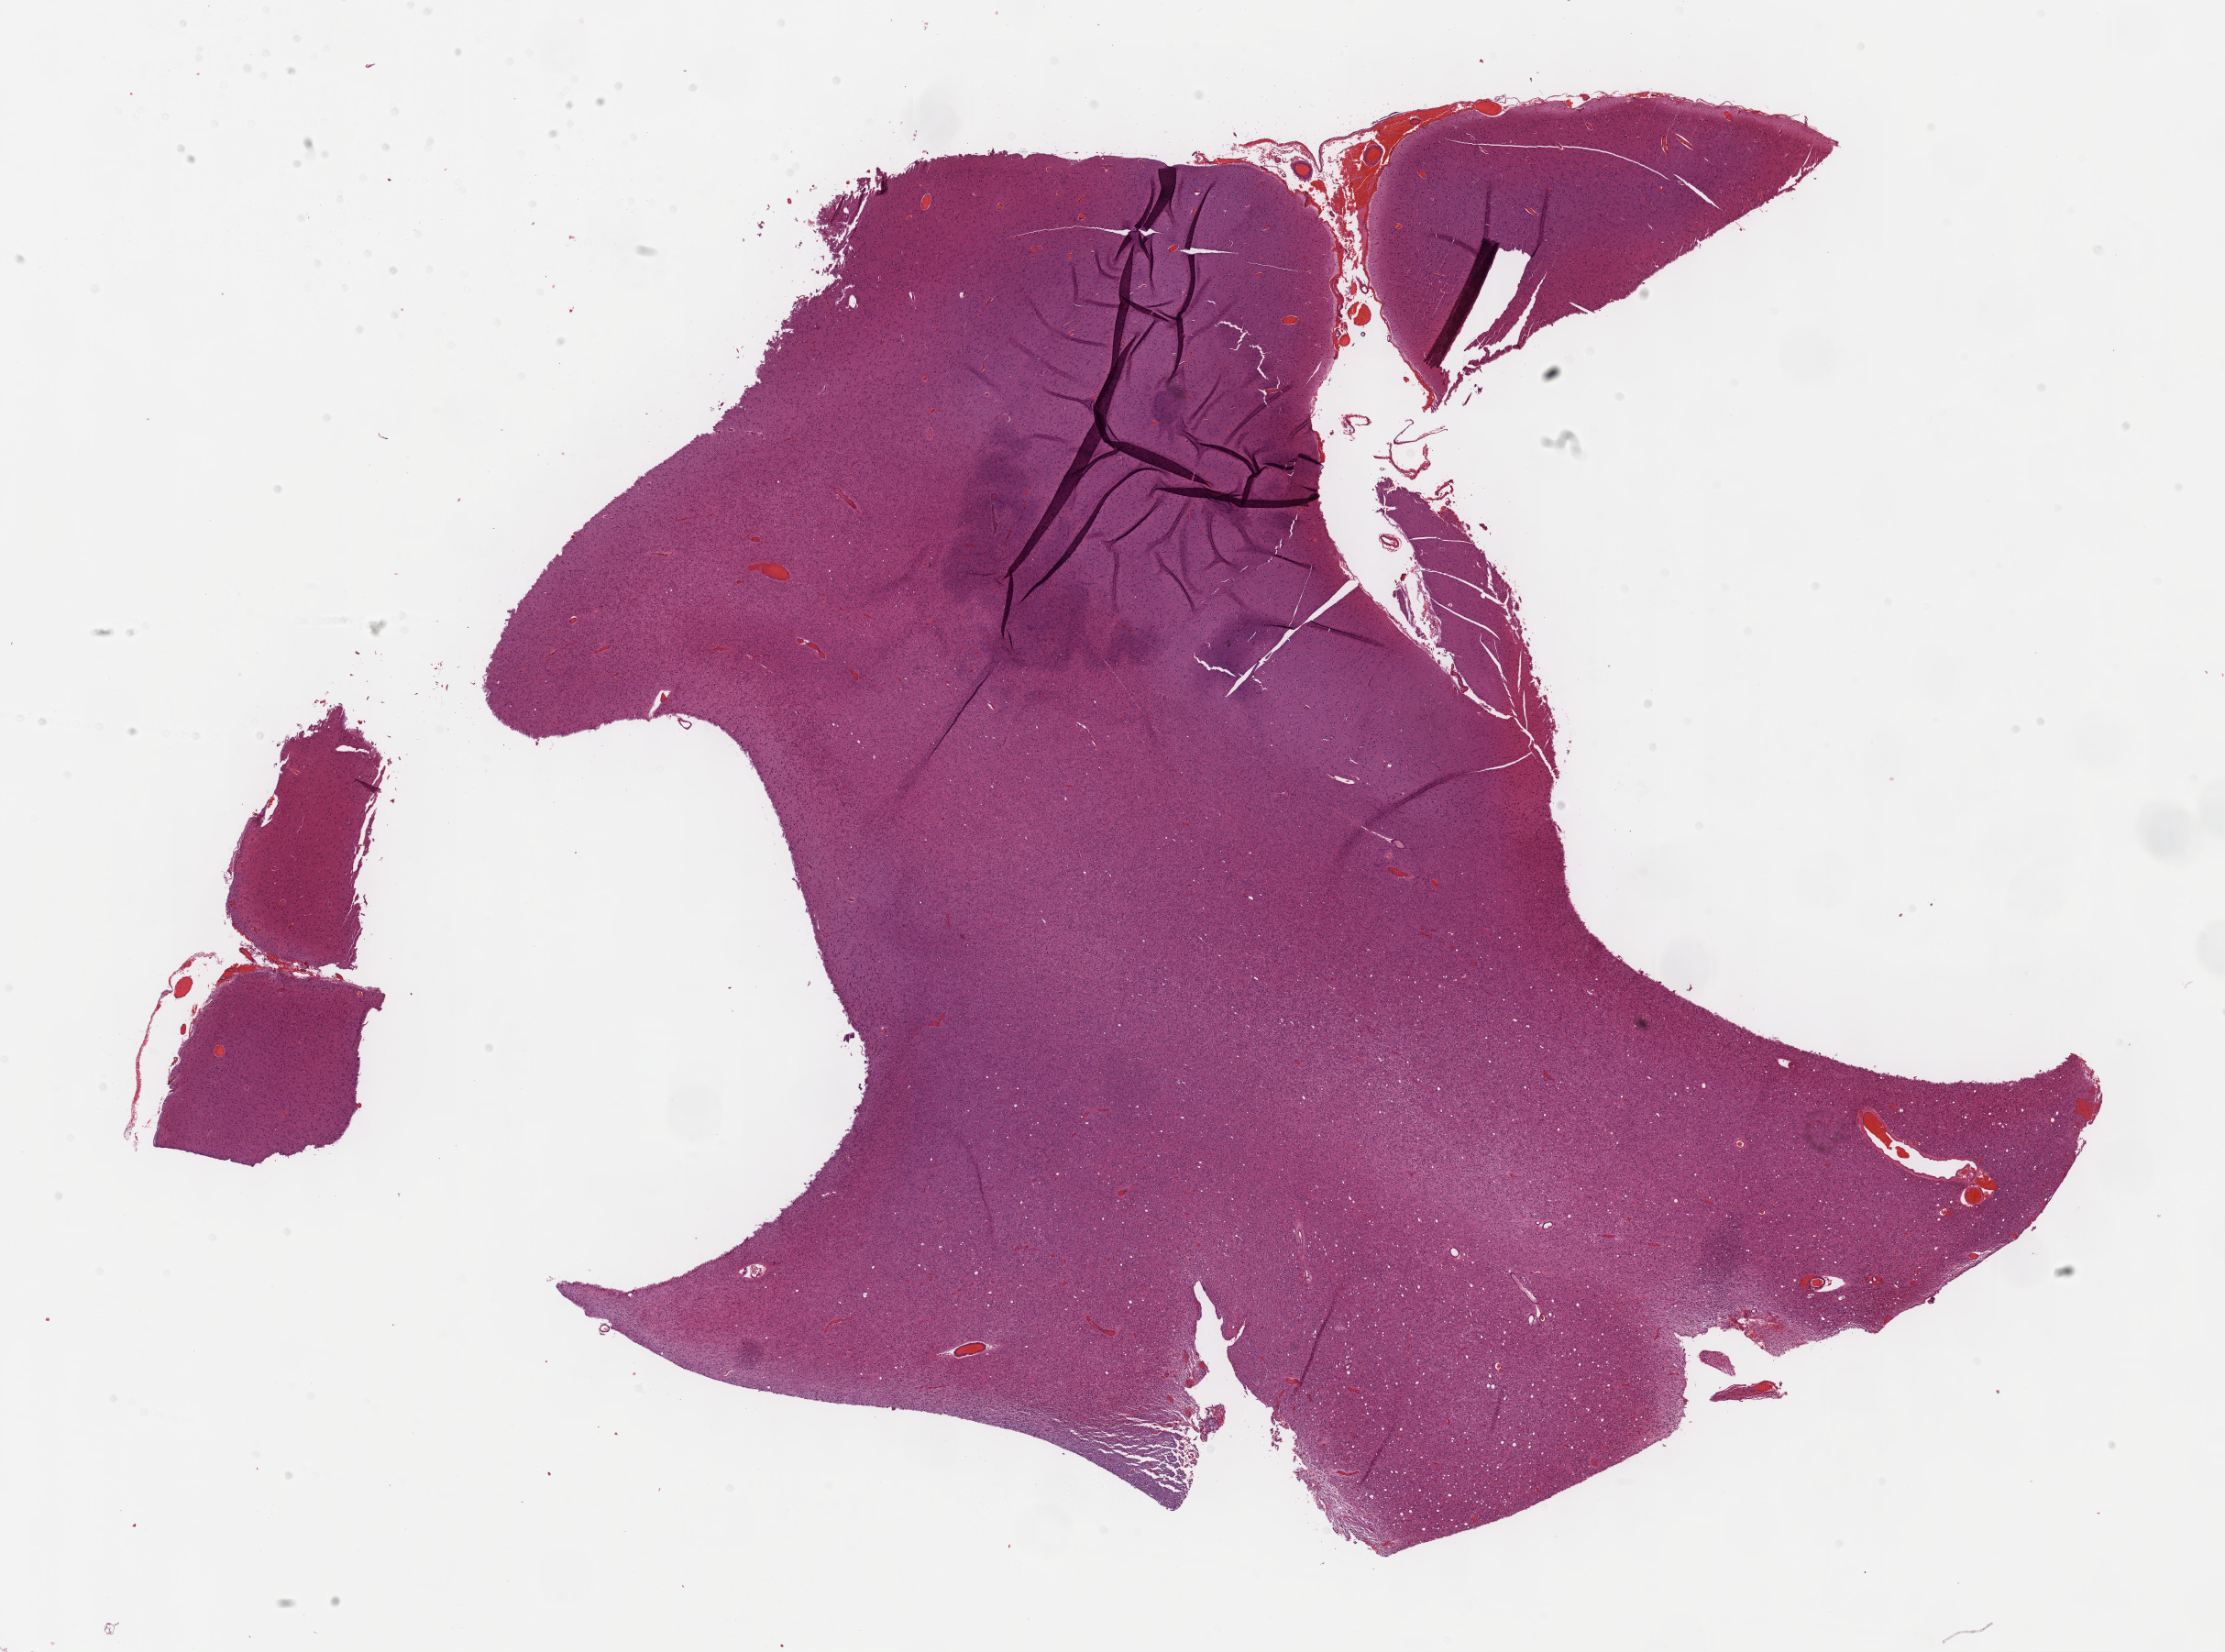
H&E-stained whole-slide image, low-resolution overview of the scanned area, about 19.6 x 14.6 mm (slide scanned at 40x). Formalin-fixed paraffin-embedded (FFPE) diagnostic section. Sample: primary tumour, brain. Male patient; age at initial diagnosis 33 years. Histologic grade: G2 (moderately differentiated).
* laterality: right
* diagnosis: Oligodendroglioma, NOS